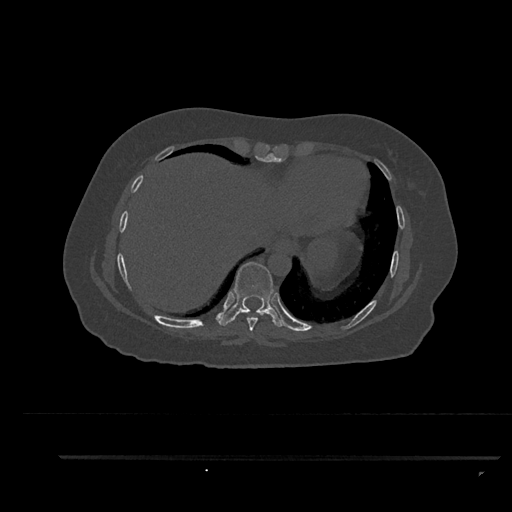
CT including the spine, one axial slice; slice 431 of 797 in the series (ordered by position); reconstruction kernel Br40s/3; bone window (W 1800 / L 400 HU); 512 × 512 image matrix. Patient: female, 44 years. Case-level facts recorded for this patient, not image findings: primary cancer: renal; vertebrae with lytic lesions (as recorded): L1.
Annotated regions visible in this slice (semi-automatically segmented with operator editing):
- T8 vertebra: bounding box <244,310,264,331> (left, top, right, bottom; pixels)
- T9 vertebra: <218,262,286,327>